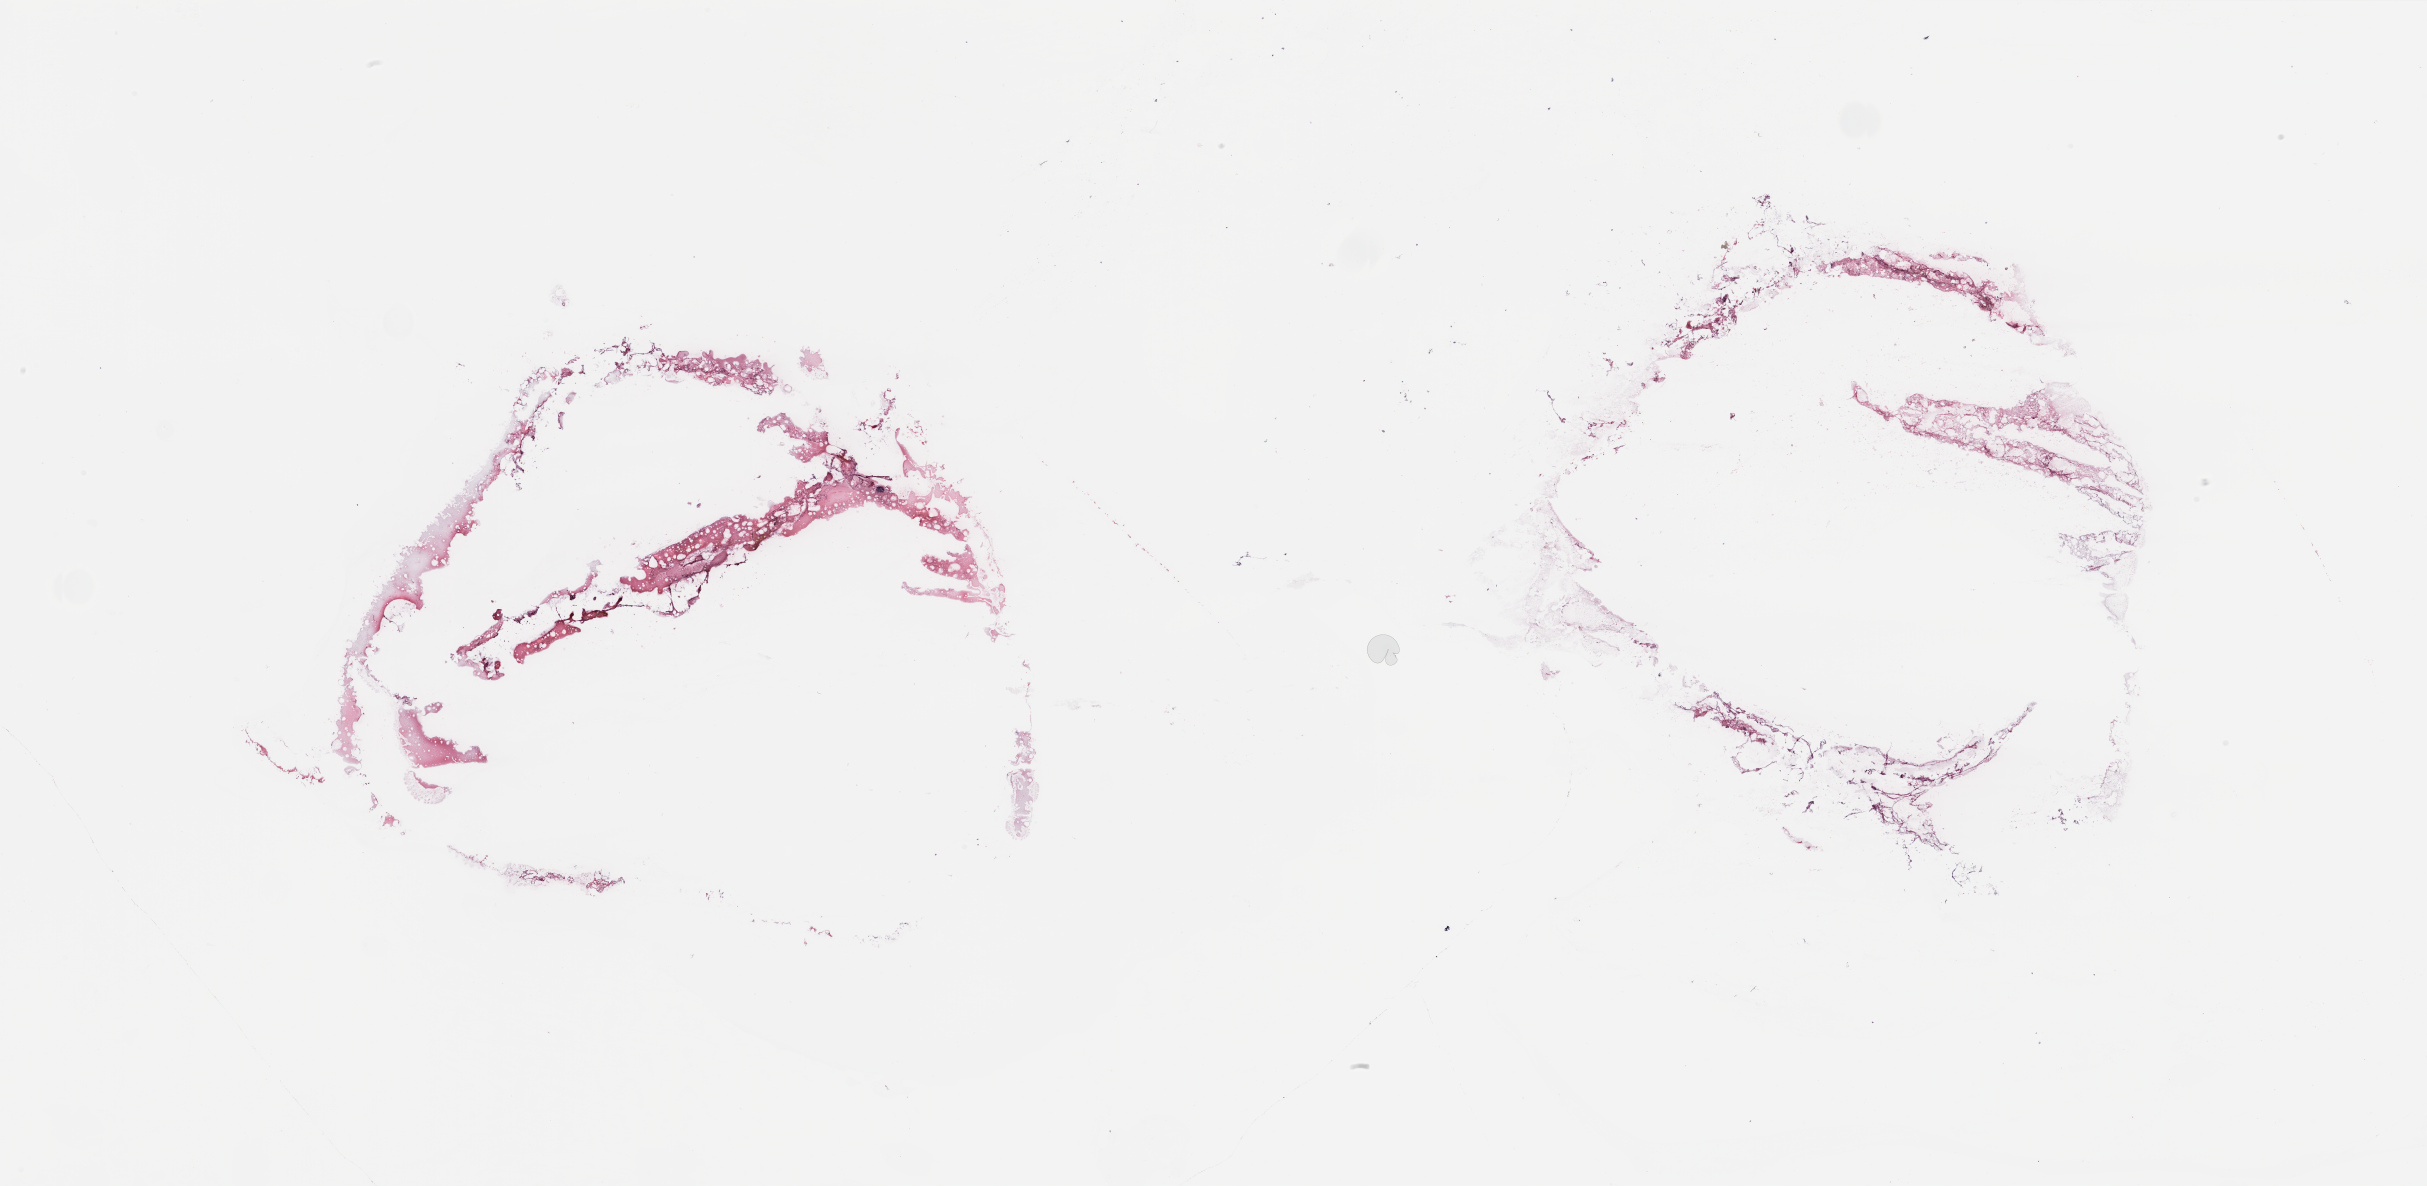
Digitized Hematoxylin and eosin (H&E) stained tissue section (whole slide) — shown as a low-resolution overview of the whole scanned area (about 38.4 x 18.8 mm, acquisition: 20x scan); breast, tissue type not recorded.
• patient diagnosis (cohort enrolment): breast cancer (breast)